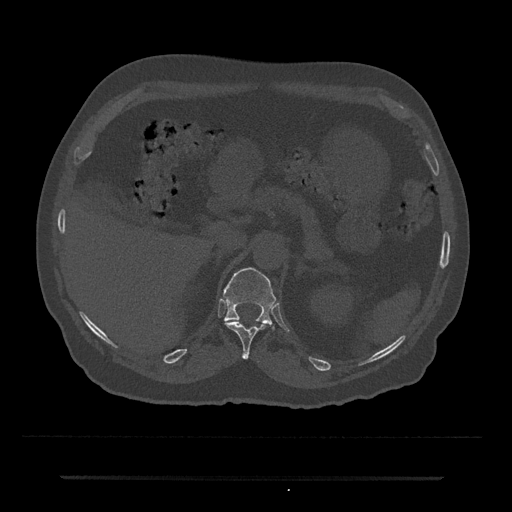
CT including the spine, one axial slice; slice 152 of 797 in the series (ordered by position); reconstruction kernel Br40s/3; 120 kVp; bone window (W 1800 / L 400 HU); 512 × 512 image matrix. Male patient, age 69 years. From the clinical record (not read from this slice): primary cancer: prostate.
Outlined on this slice (semi-automatic segmentation, software-assisted and operator-edited):
- T11 vertebra: box from (x=225, y=321) to (x=266, y=359) px
- T12 vertebra: (x=223, y=267)–(x=276, y=325)